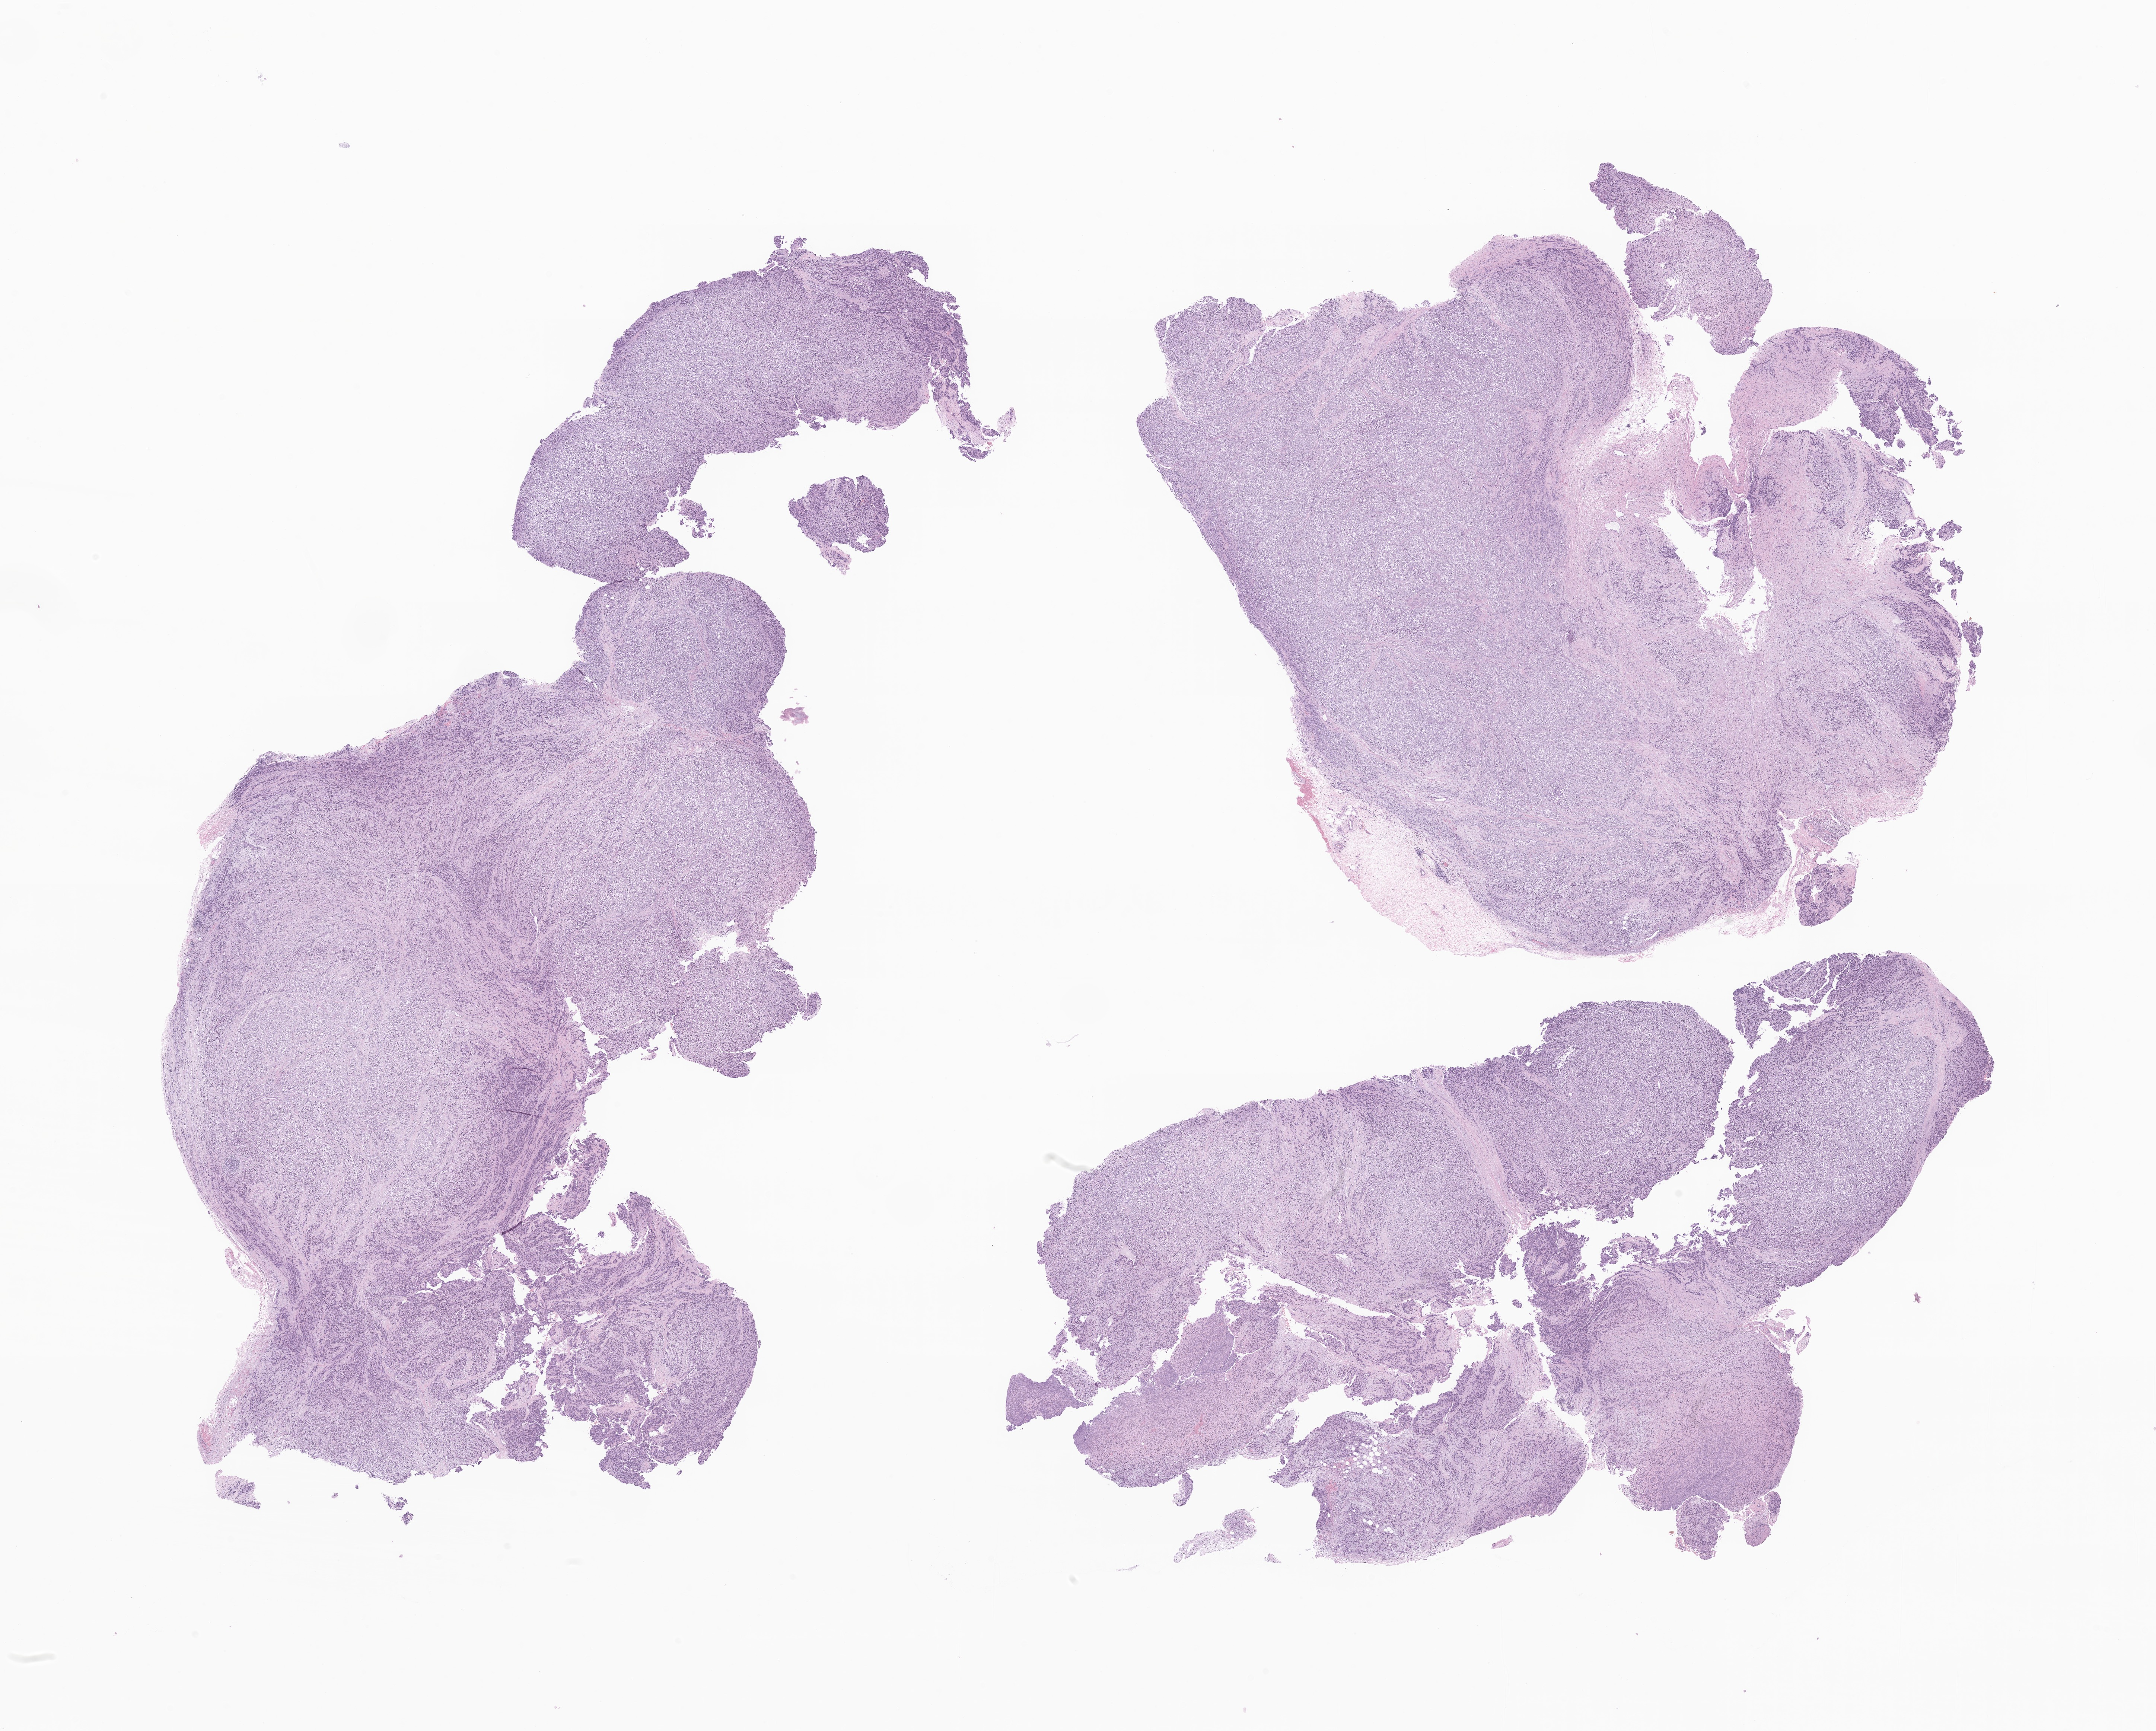
Haematoxylin and eosin whole-slide image of tumor tissue from the eyelid, low-resolution overview of the scanned area, about 24.4 x 19.6 mm, FFPE section. Female patient, age 154 months (12 years 10 months).
Recorded diagnosis: Spindle cell rhabdomyosarcoma.